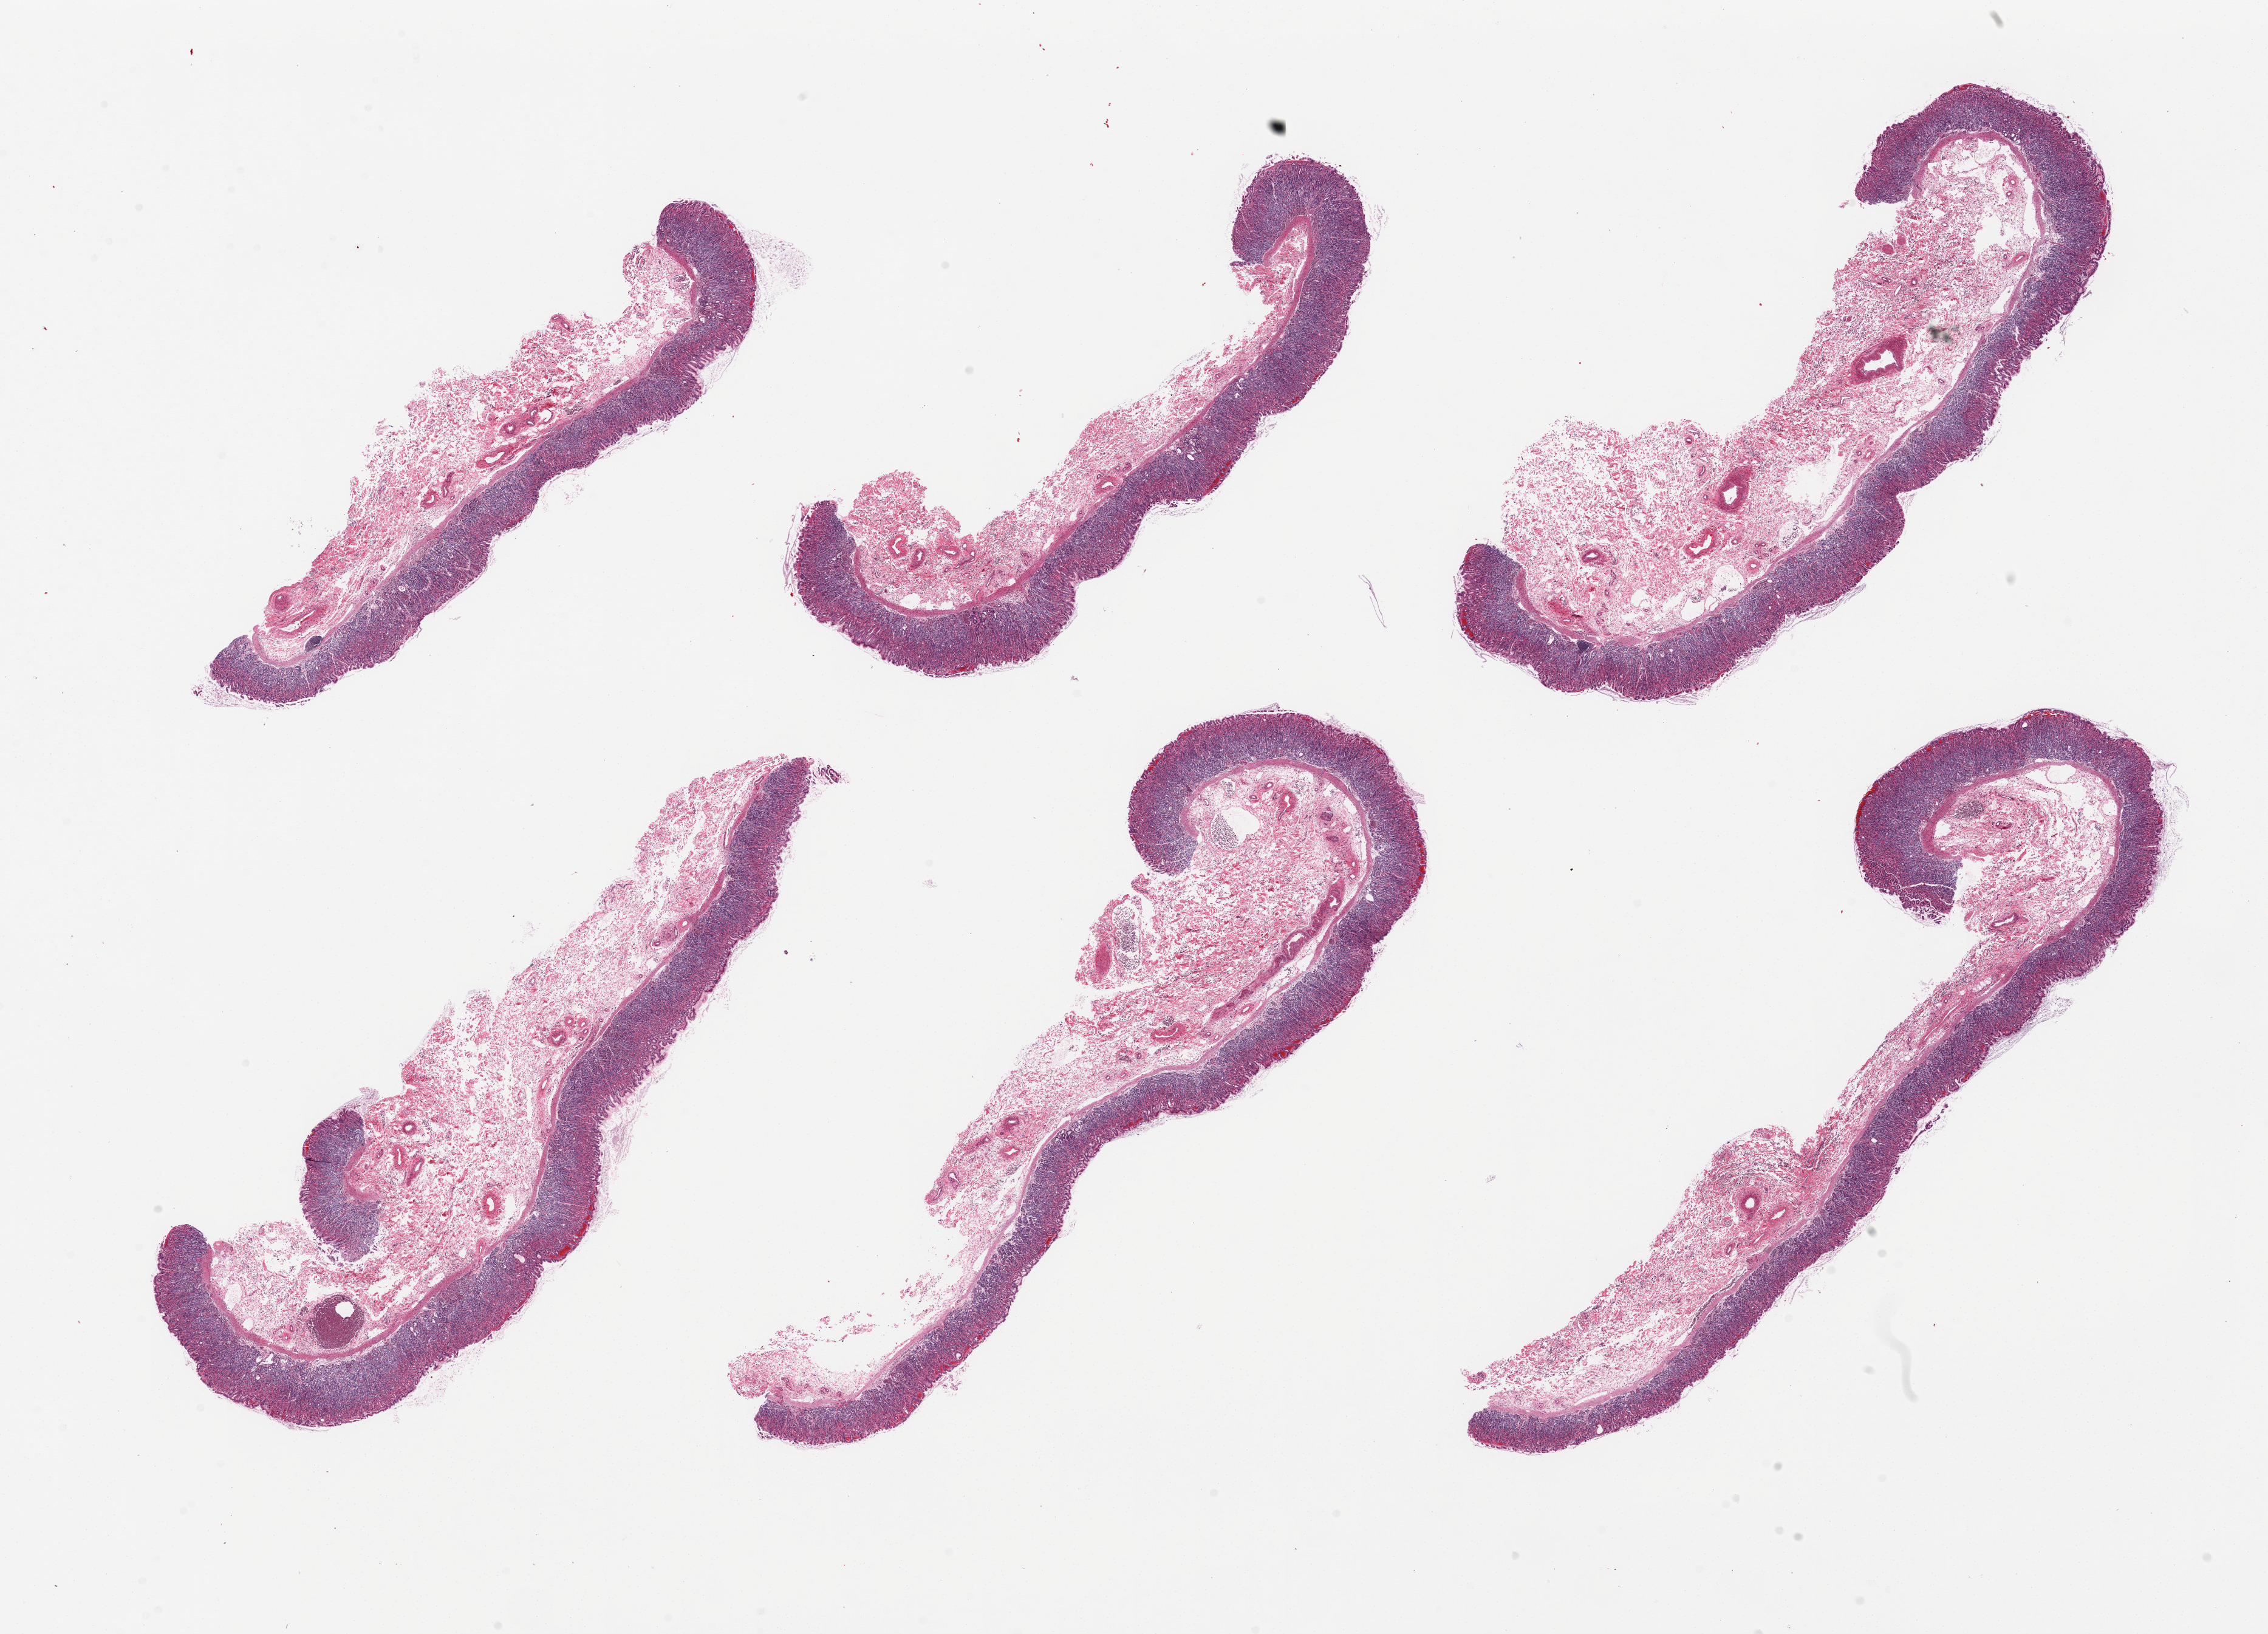
Whole-slide image, haematoxylin and eosin stain — shown as a low-resolution overview of the whole scanned area (about 29.5 x 21.3 mm, acquisition: 20x scan). PAXgene-fixed paraffin-embedded (PFPE) section. Section of stomach (target tissue). Donor tissue sample. Male donor.
* reviewer comment on this tissue sample: 6 pieces, well preserved mucoa; patchy acute/active gastritis with leukocytes in deep mucosa and submucosa; Mucosa up to ~0.5-0.7mm thick, ~20% total